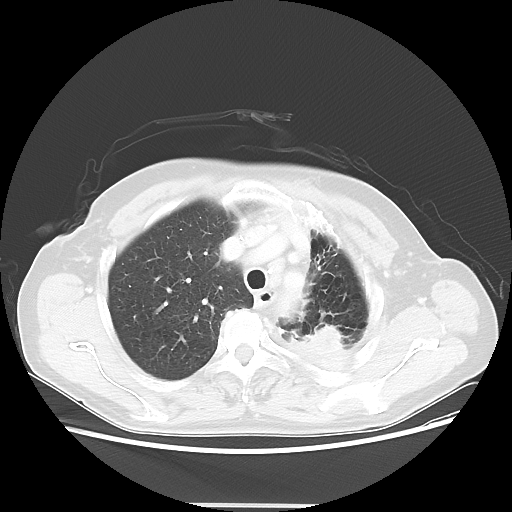
Chest CT, one axial slice; slice 42 of 56 in the series (ordered by position); reconstruction kernel LUNG; 100 kVp; lung window (W 1500 / L -600 HU); 512 × 512 image matrix. Female patient, age 63 years. From the clinical record (not read from this slice): clinical TNM (as recorded): T2a N0 M0.
Outlined on this slice (rectangle marked by the reading radiologist):
- lung tumour (recorded histology: adenocarcinoma): bounding box (x1, y1, x2, y2) in pixels: (303, 316, 341, 359)